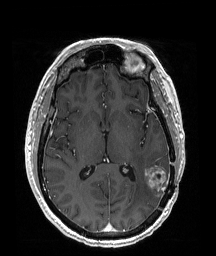
Brain MRI from a brain-tumour surgery series, one axial slice. Slice 93 of 192 in the series (ordered by position). T1-weighted post-contrast. 1 mm slice thickness. 216 × 256 image matrix, field of view 211 × 250 mm. Case-level facts recorded for this patient, not image findings: histopathology: Glioblastoma; WHO grade: 4; IDH mutation: no.
Annotated regions visible in this slice (outlined manually by an expert reader):
- tumour: bounding box [x1, y1, x2, y2] px = [144, 166, 170, 197]